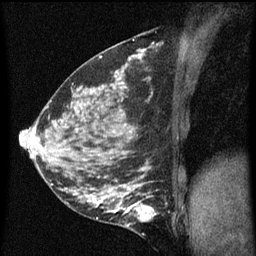
Breast MRI (dynamic contrast-enhanced), one sagittal slice. Slice 26 of 60 in the series (ordered by position). Dynamic contrast-enhanced series, image 2 of 5 at this slice position (ordered by acquisition). 1.5 T. TE 4.2 ms, TR 8 ms. 2 mm slice thickness. 256 × 256 image matrix. Female patient, age 35 years.
Outlined on this slice (semi-automatic segmentation, software-assisted and operator-edited):
- analysis volume of interest (the breast-tissue region the enhancement analysis was run in; not a lesion): bounding box [x1, y1, x2, y2] px = [118, 190, 160, 229]
- tumour enhancement mask (voxels above the 70 % enhancement threshold inside the analysis volume of interest): [118, 194, 154, 227]